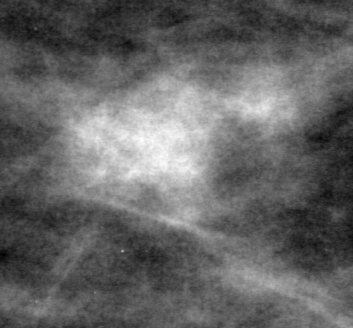
Crop from a digitized film mammogram around one marked abnormality; right breast; CC view; BI-RADS breast density category 3 (scale 1–4).
Mass, shape oval, margins circumscribed; BI-RADS assessment category 4; subtlety rating 3 on a 1 (subtle) to 5 (obvious) scale; pathology result (as recorded, not read from the image): benign.